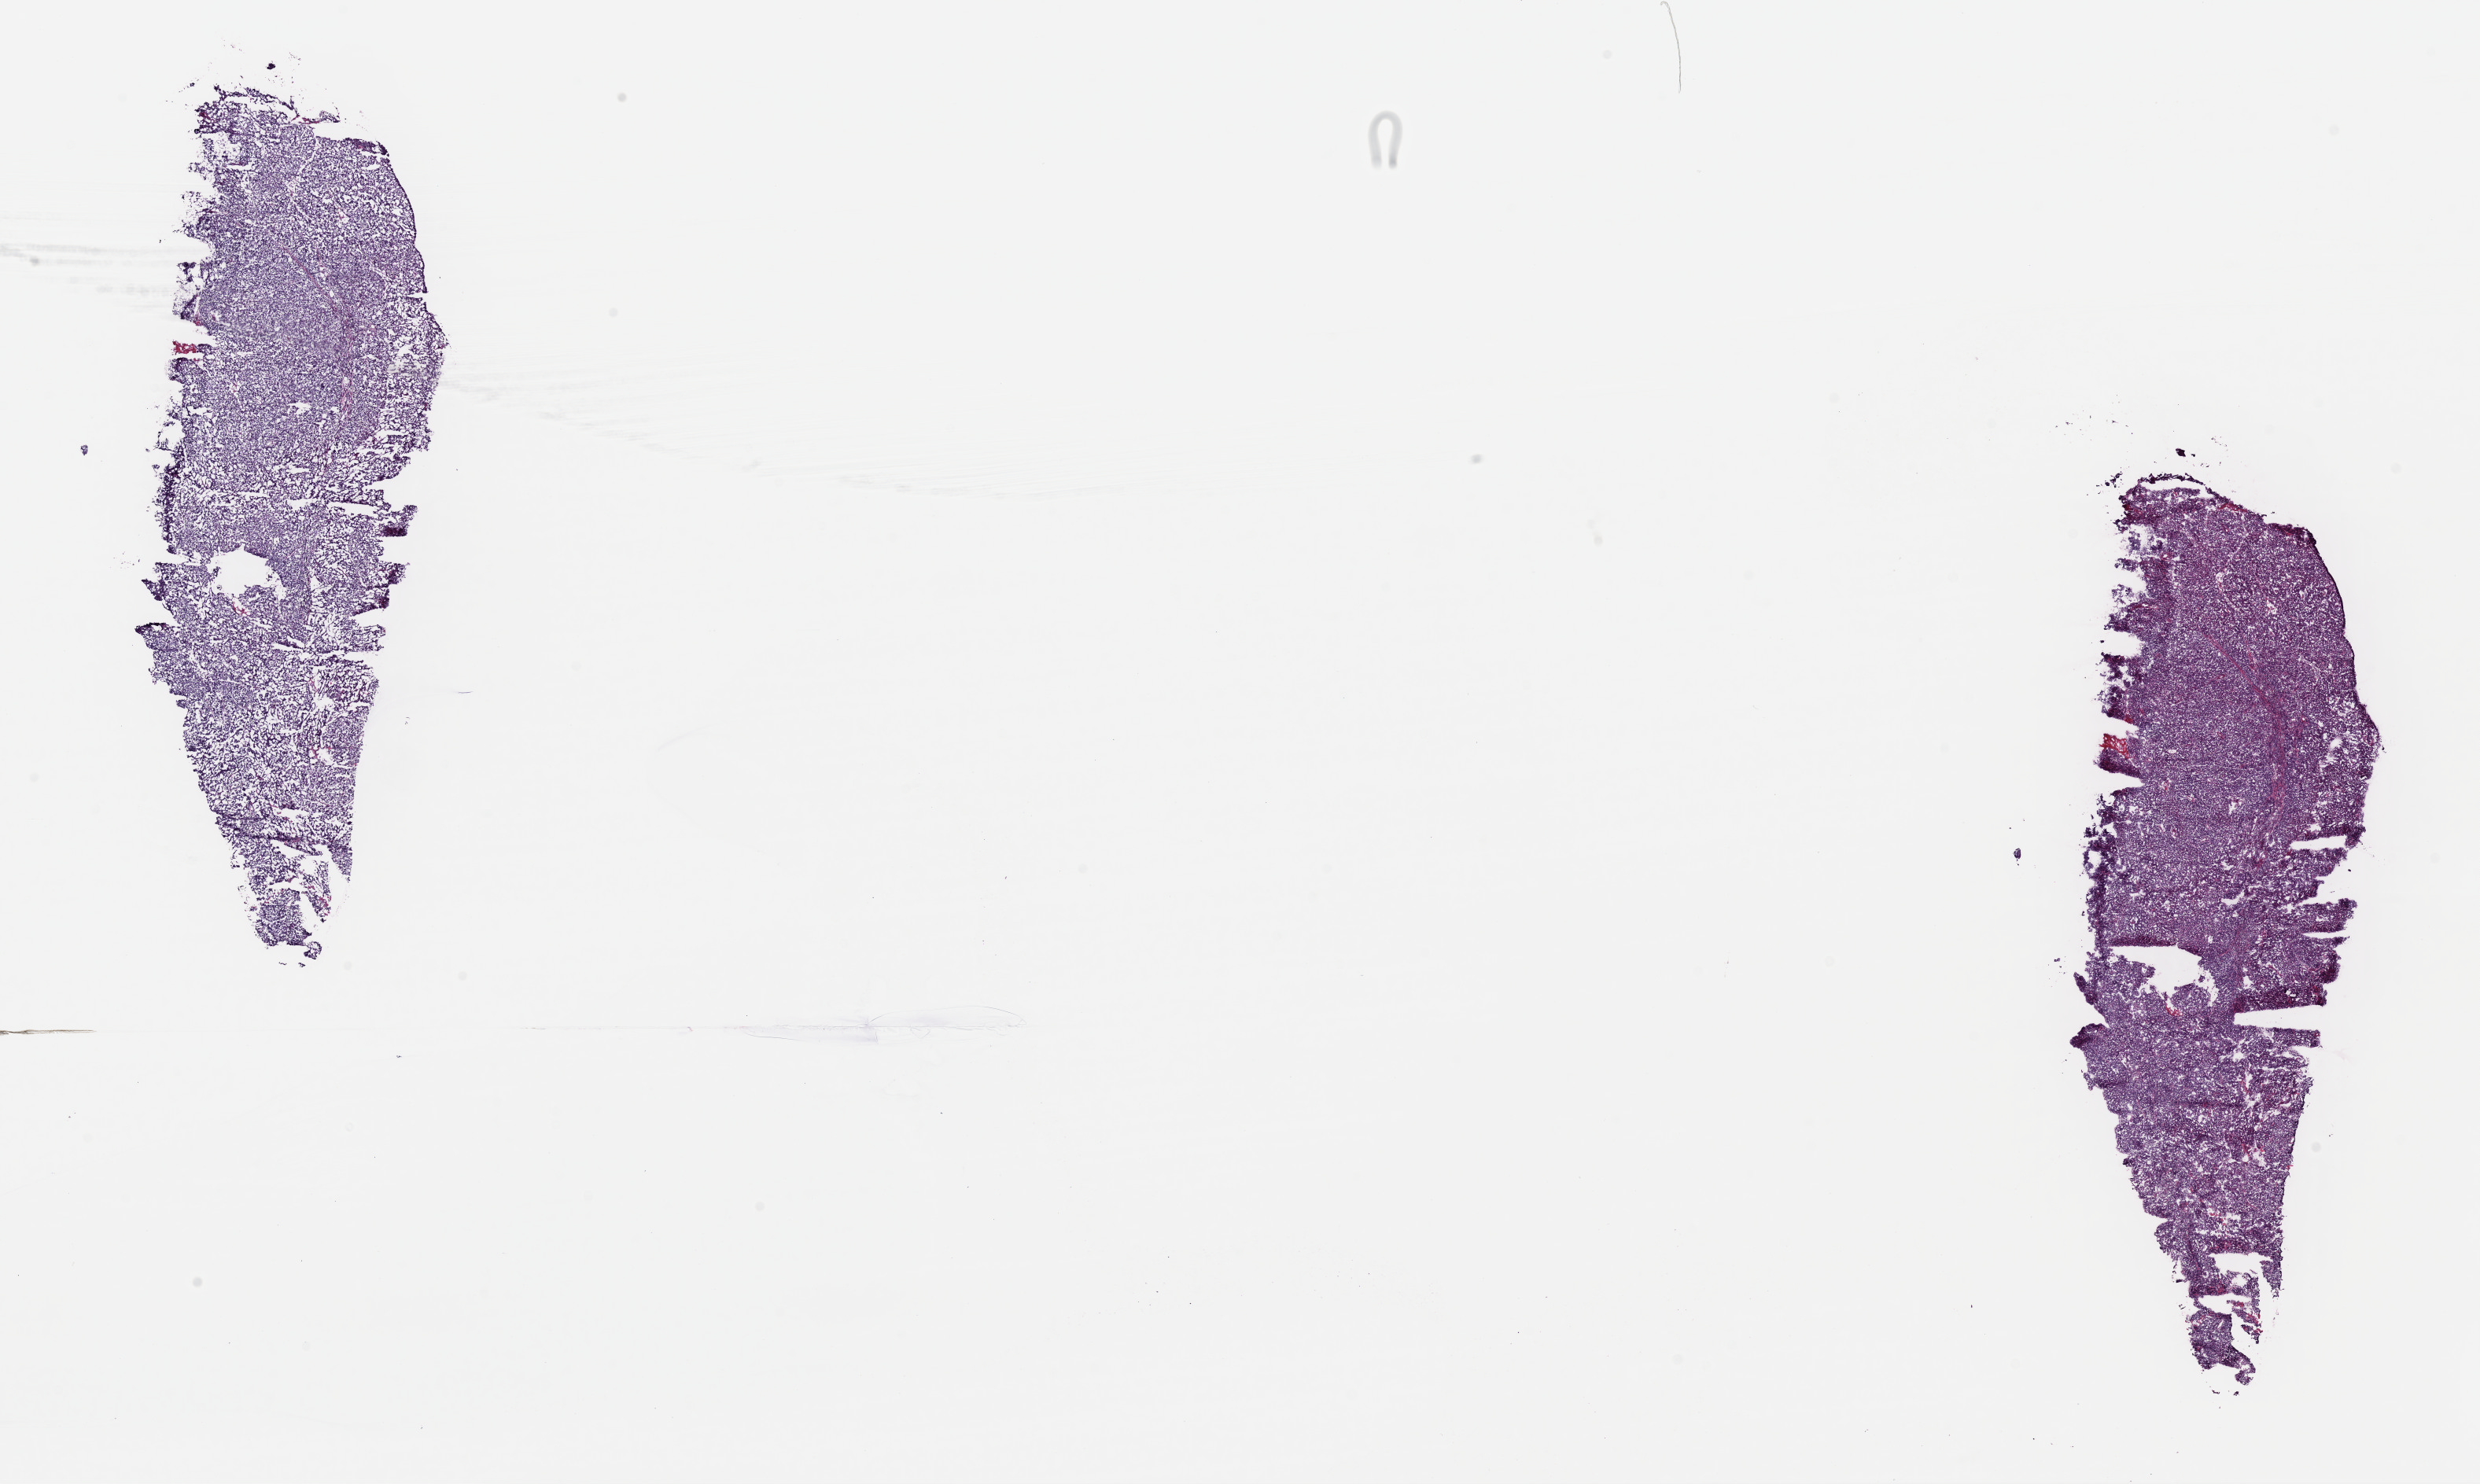
Whole-slide histology image, H&E-stained — a low-resolution overview of the entire scanned area, about 24.9 x 14.9 mm (acquisition: 40x scan), frozen section from the top of the tissue portion, sample: primary tumour, uterus. Female patient; age at initial diagnosis 65 years. Histologic grade: G3 (poorly differentiated). Pathologist review of this section (percent, as recorded): tumour cells 95%, tumour nuclei 96%, normal cells 0%, stromal cells 5%, necrosis 0%. Infiltration values recorded for this section: lymphocyte infiltration 3%, monocyte infiltration 0%, neutrophil infiltration 0%.
Pathologic diagnosis: Endometrioid adenocarcinoma, NOS (endometrium). FIGO stage: IA. Lymph nodes positive (case pathology): 0 of 7 examined.